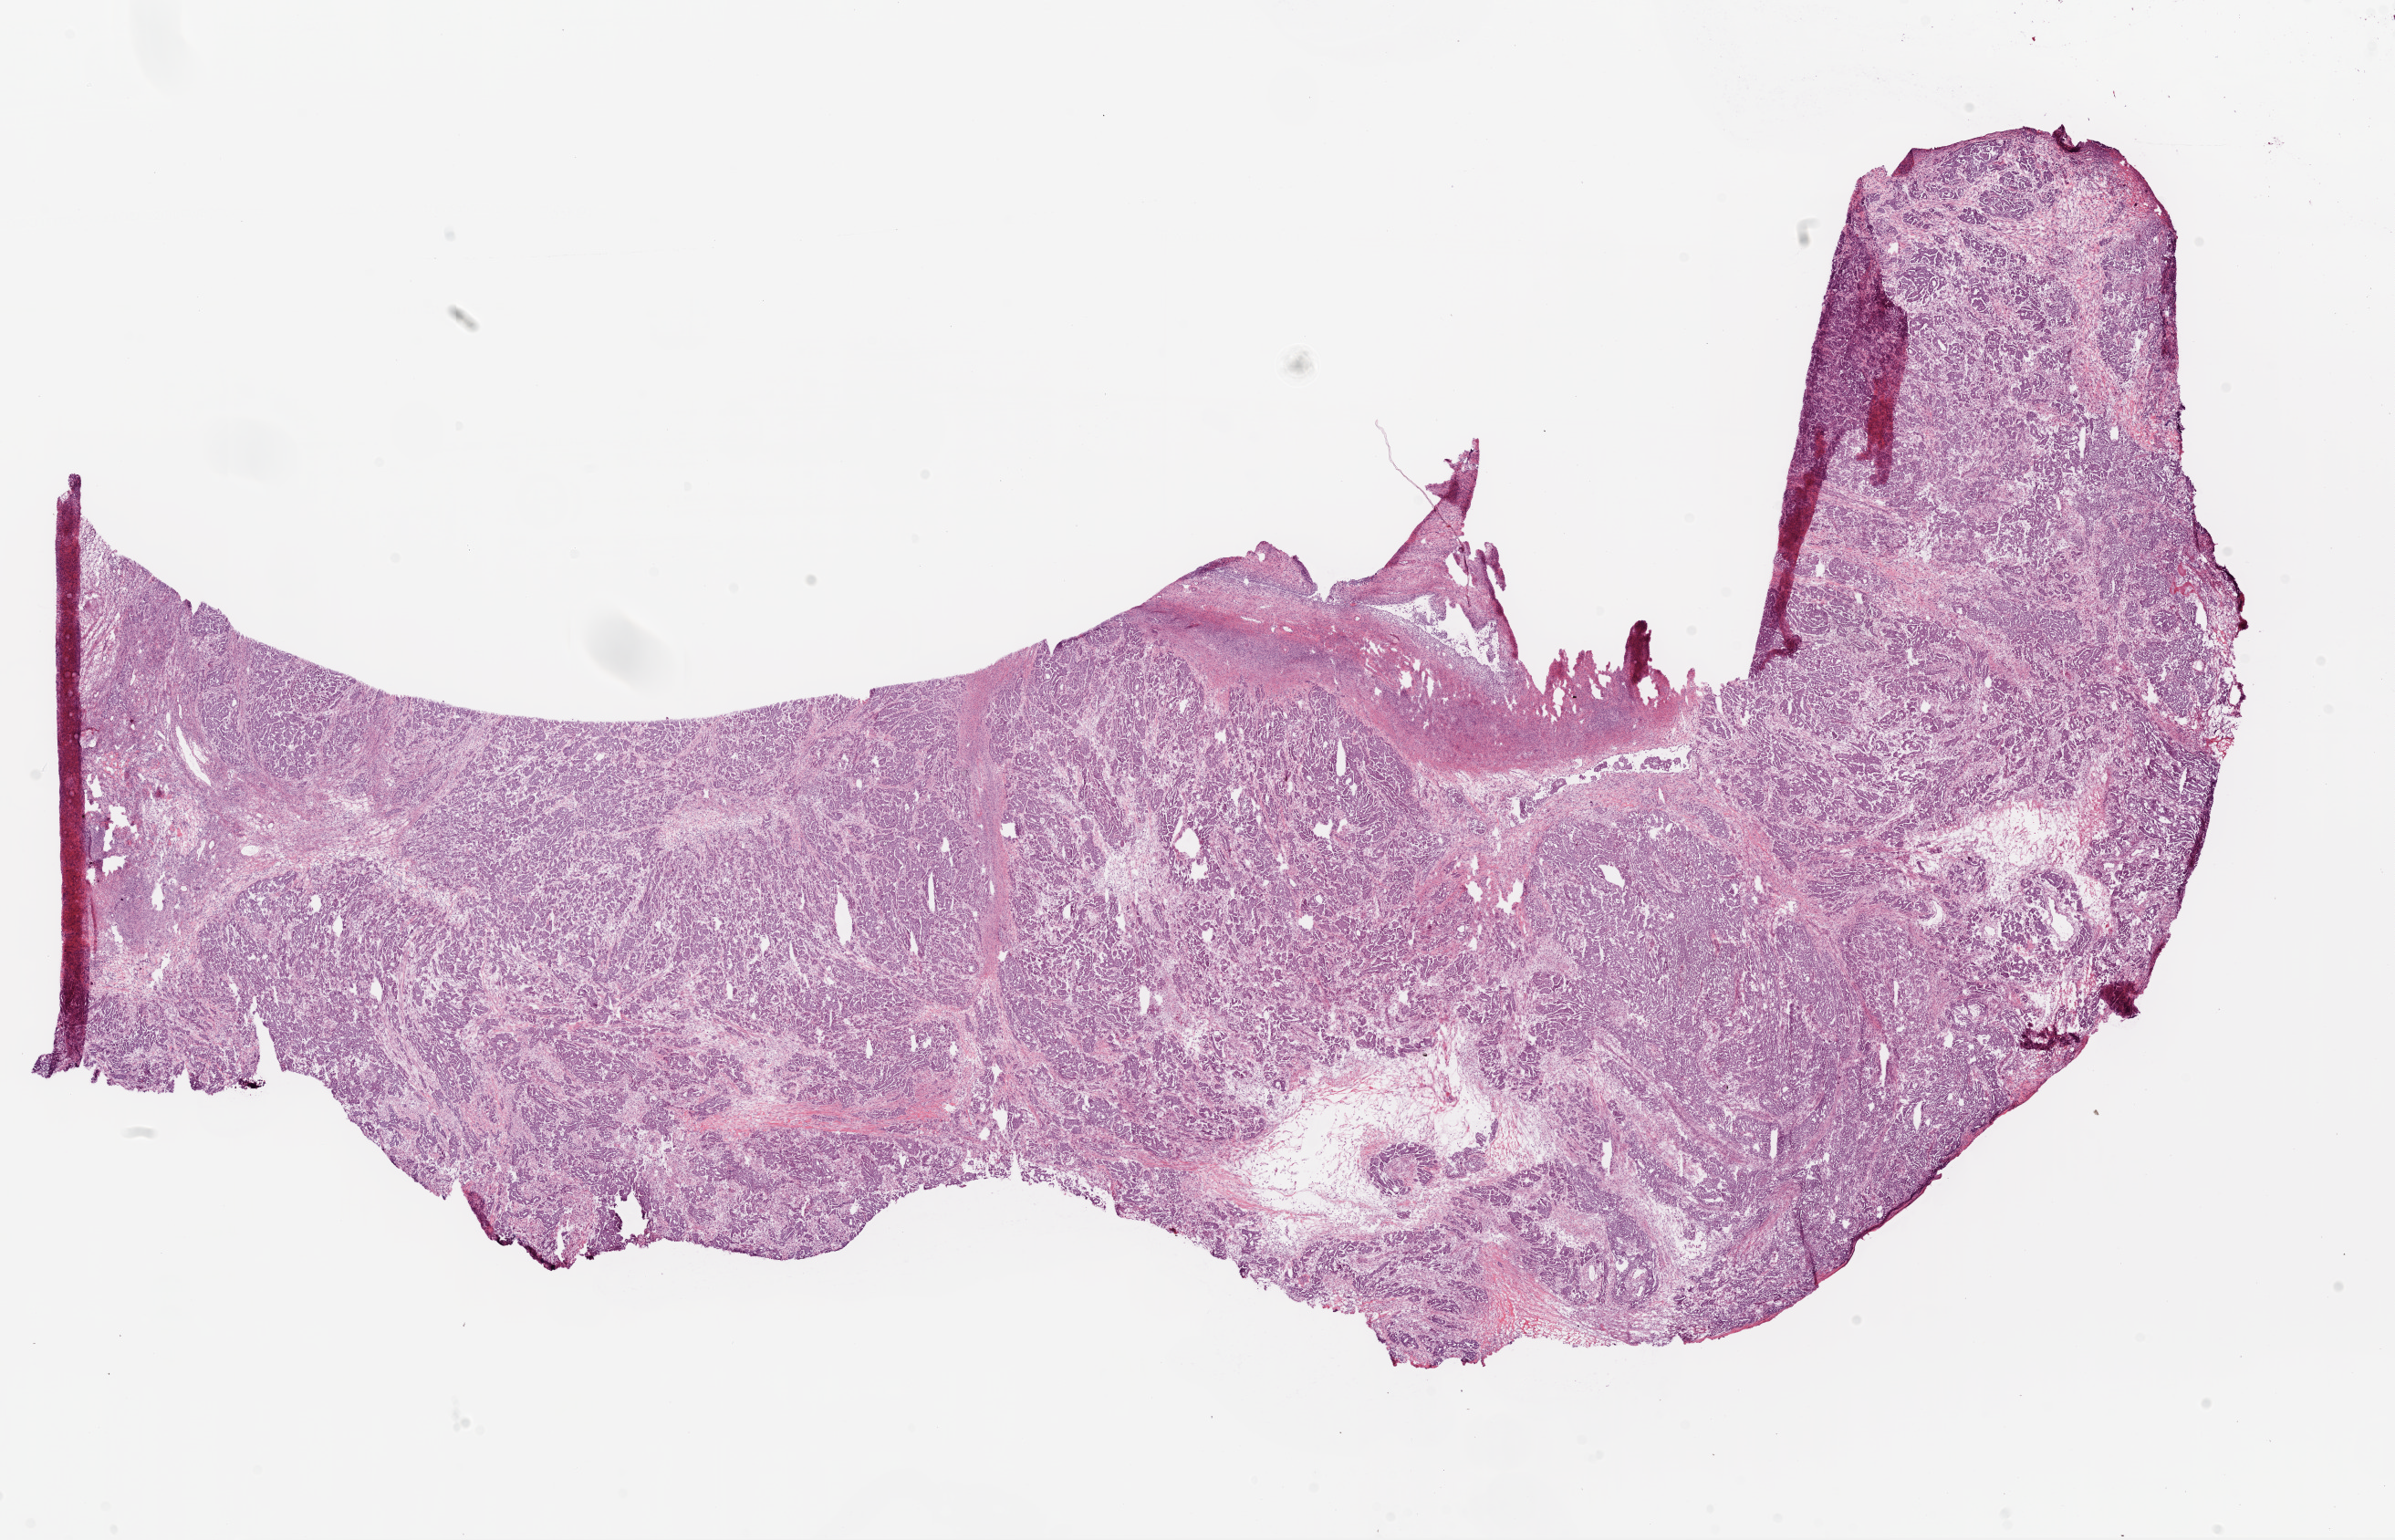
H&E whole-slide image, low-resolution overview of the scanned area, about 21.1 x 13.5 mm (from a 20x scan). Frozen section from the bottom of the tissue portion. Primary tumour sample from the ovary. Female, age 38 years at initial diagnosis. Histologic grade: G3 (poorly differentiated). Pathologist review of this section (percent, as recorded): tumour cells 85%, tumour nuclei 85%, normal cells 1%, stromal cells 14%, necrosis 0%.
• FIGO stage: IIIC
• laterality: bilateral
• histologic diagnosis: Serous cystadenocarcinoma, NOS